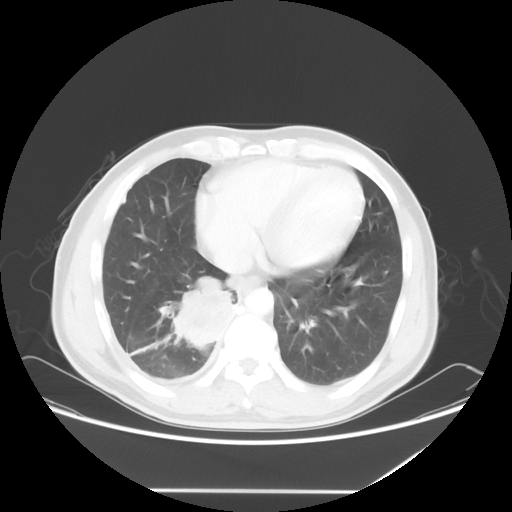
Chest CT, one axial slice. Slice 21 of 60 in the series (ordered by position). Reconstruction kernel STANDARD. 120 kVp. Lung window (W 1500 / L -600 HU). 512 × 512 image matrix, field of view 419 × 419 mm. Patient: male, 48 years. From the clinical record (not read from this slice): clinical TNM (as recorded): T3 N3 M1a.
Annotated regions visible in this slice (rectangle marked by the reading radiologist):
- lung tumour (recorded histology: squamous cell carcinoma): bounding box (x1, y1, x2, y2) in pixels: (160, 271, 237, 355)